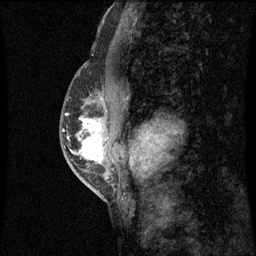
Breast MRI (dynamic contrast-enhanced), one sagittal slice; slice 32 of 60 in the series (ordered by position); dynamic contrast-enhanced series, image 2 of 3 at this slice position (ordered by acquisition); 1.5 T; TE 4.2 ms, TR 8.9 ms; 2 mm slice thickness; 256 × 256 image matrix, field of view 200 × 200 mm. Patient: female, 50 years. Case-level facts recorded for this patient, not image findings: setting: breast cancer imaged before/during neoadjuvant chemotherapy; receptor status: triple-negative.
Outlined on this slice (semi-automatically segmented with operator editing):
- analysis volume of interest (the breast-tissue region the enhancement analysis was run in; not a lesion): bounding box [x1, y1, x2, y2] px = [68, 86, 106, 169]
- tumour enhancement mask (voxels above the 70 % enhancement threshold inside the analysis volume of interest): [82, 118, 103, 163]